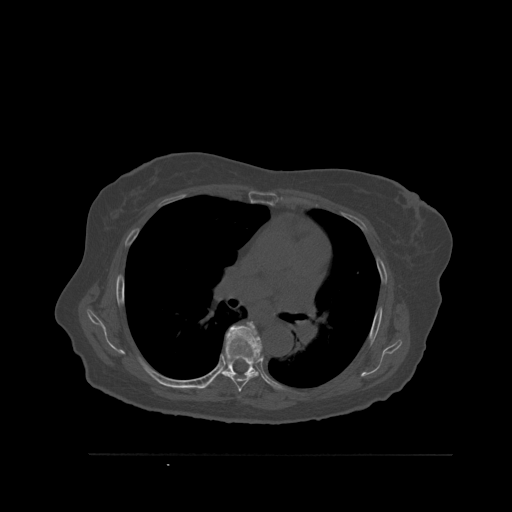
CT including the spine, one axial slice; position 374 of 527 along the scan axis; bone window (W 1800 / L 400 HU); 512 × 512 image matrix, field of view 470 × 470 mm. Patient: female, 73 years. Case-level facts recorded for this patient, not image findings: primary cancer: breast.
Structures marked on this image (semi-automatically segmented with operator editing):
- T6 vertebra: bounding box <223,351,262,392> (left, top, right, bottom; pixels)
- T7 vertebra: <207,322,262,386>